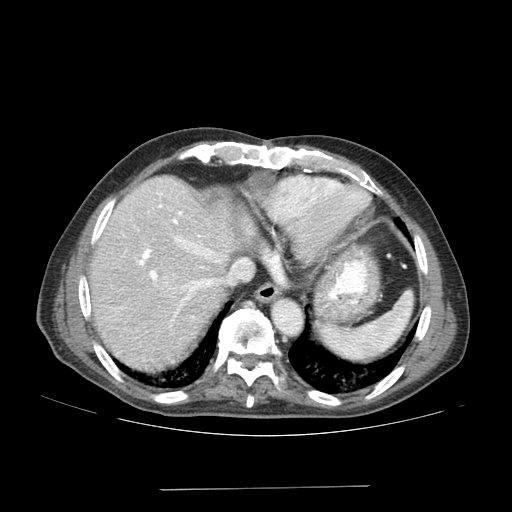
Contrast-enhanced abdominal CT (liver protocol), one axial slice. Position 142 of 192 along the scan axis. Reconstruction kernel SOFT. 120 kVp. Soft-tissue window (W 400 / L 40 HU). 512 × 512 image matrix, field of view 400 × 400 mm. From the clinical record (not read from this slice): diagnosis: hepatocellular carcinoma (patient treated with transarterial chemoembolisation; whether this scan precedes or follows treatment is not stated here); TNM stage (as recorded): Stage-IVA; Child-Pugh class: A; tumour differentiation: poorly differentiated; tumour nodularity: uninodular.
Structures marked on this image (semi-automatic segmentation, software-assisted and operator-edited):
- liver parenchyma outside the tumour (the mass and vessels are separate outlines, so this box may not span the whole liver): box from (x=90, y=176) to (x=254, y=370) px
- mass: (x=153, y=271)–(x=181, y=301)
- liver vessels: (x=138, y=193)–(x=220, y=315)